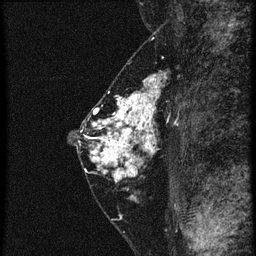
Breast MRI (dynamic contrast-enhanced), one sagittal slice; slice 31 of 60 in the series (ordered by position); 4 images stored at this slice position (order not interpretable as contrast timing); 1.5 T; TE 4.2 ms, TR 20.4 ms; 1.5 mm slice thickness; 256 × 256 image matrix. Female patient, age 46 years. From the clinical record (not read from this slice): setting: breast cancer imaged before/during neoadjuvant chemotherapy; receptor status: triple-negative.
Annotated regions visible in this slice (semi-automatically segmented with operator editing):
- analysis volume of interest (the breast-tissue region the enhancement analysis was run in; not a lesion): bounding box [x1, y1, x2, y2] px = [88, 82, 173, 185]
- tumour enhancement mask (voxels above the 90 % enhancement threshold inside the analysis volume of interest): [90, 82, 161, 183]